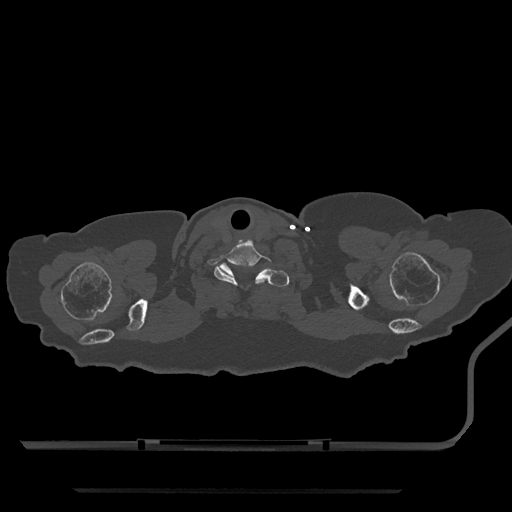
CT including the spine, one axial slice; position 728 of 797 along the scan axis; reconstruction kernel Br40s/3; 120 kVp; bone window (W 1800 / L 400 HU); 0.5 mm slice thickness; 512 × 512 image matrix, field of view 440 × 440 mm. Female patient, age 51 years. From the clinical record (not read from this slice): primary cancer: neuro; vertebrae with lytic lesions (as recorded): T8.
Annotated regions visible in this slice (semi-automatically segmented with operator editing):
- T1 vertebra: bounding box (x1, y1, x2, y2) in pixels: (219, 263, 290, 287)